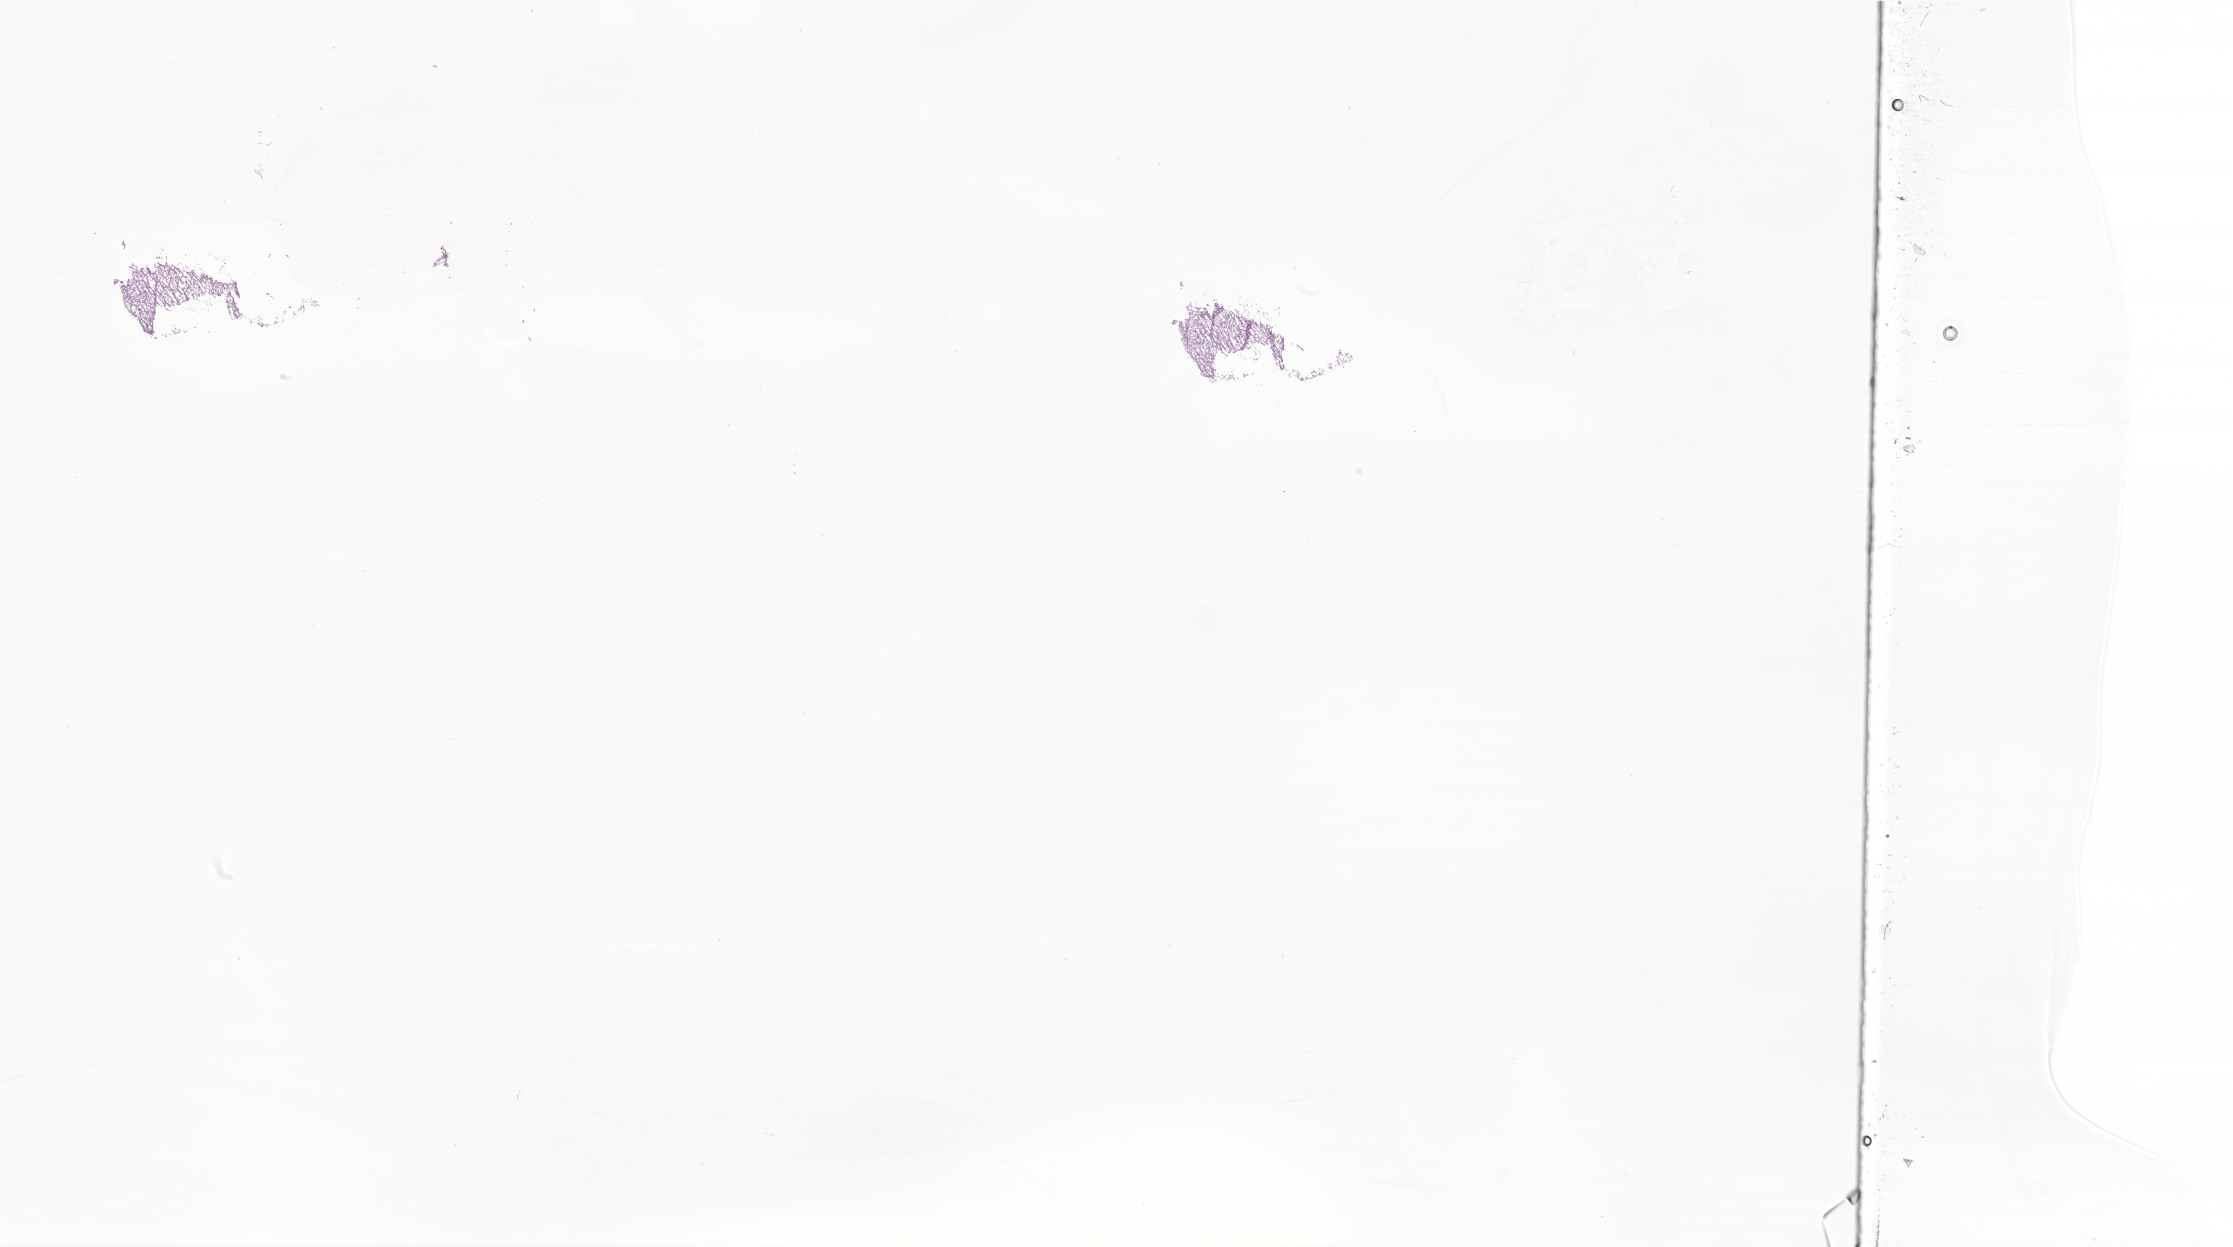
Digitized hematoxylin and eosin (H&E)-stained section of tumor tissue from the frontal lobe — low-resolution overview of the scanned area, about 37.7 x 21.0 mm, frozen section (OCT-embedded). Patient: male, age 48 months (4 years).
Diagnosis: Atypical teratoid/rhabdoid tumor.